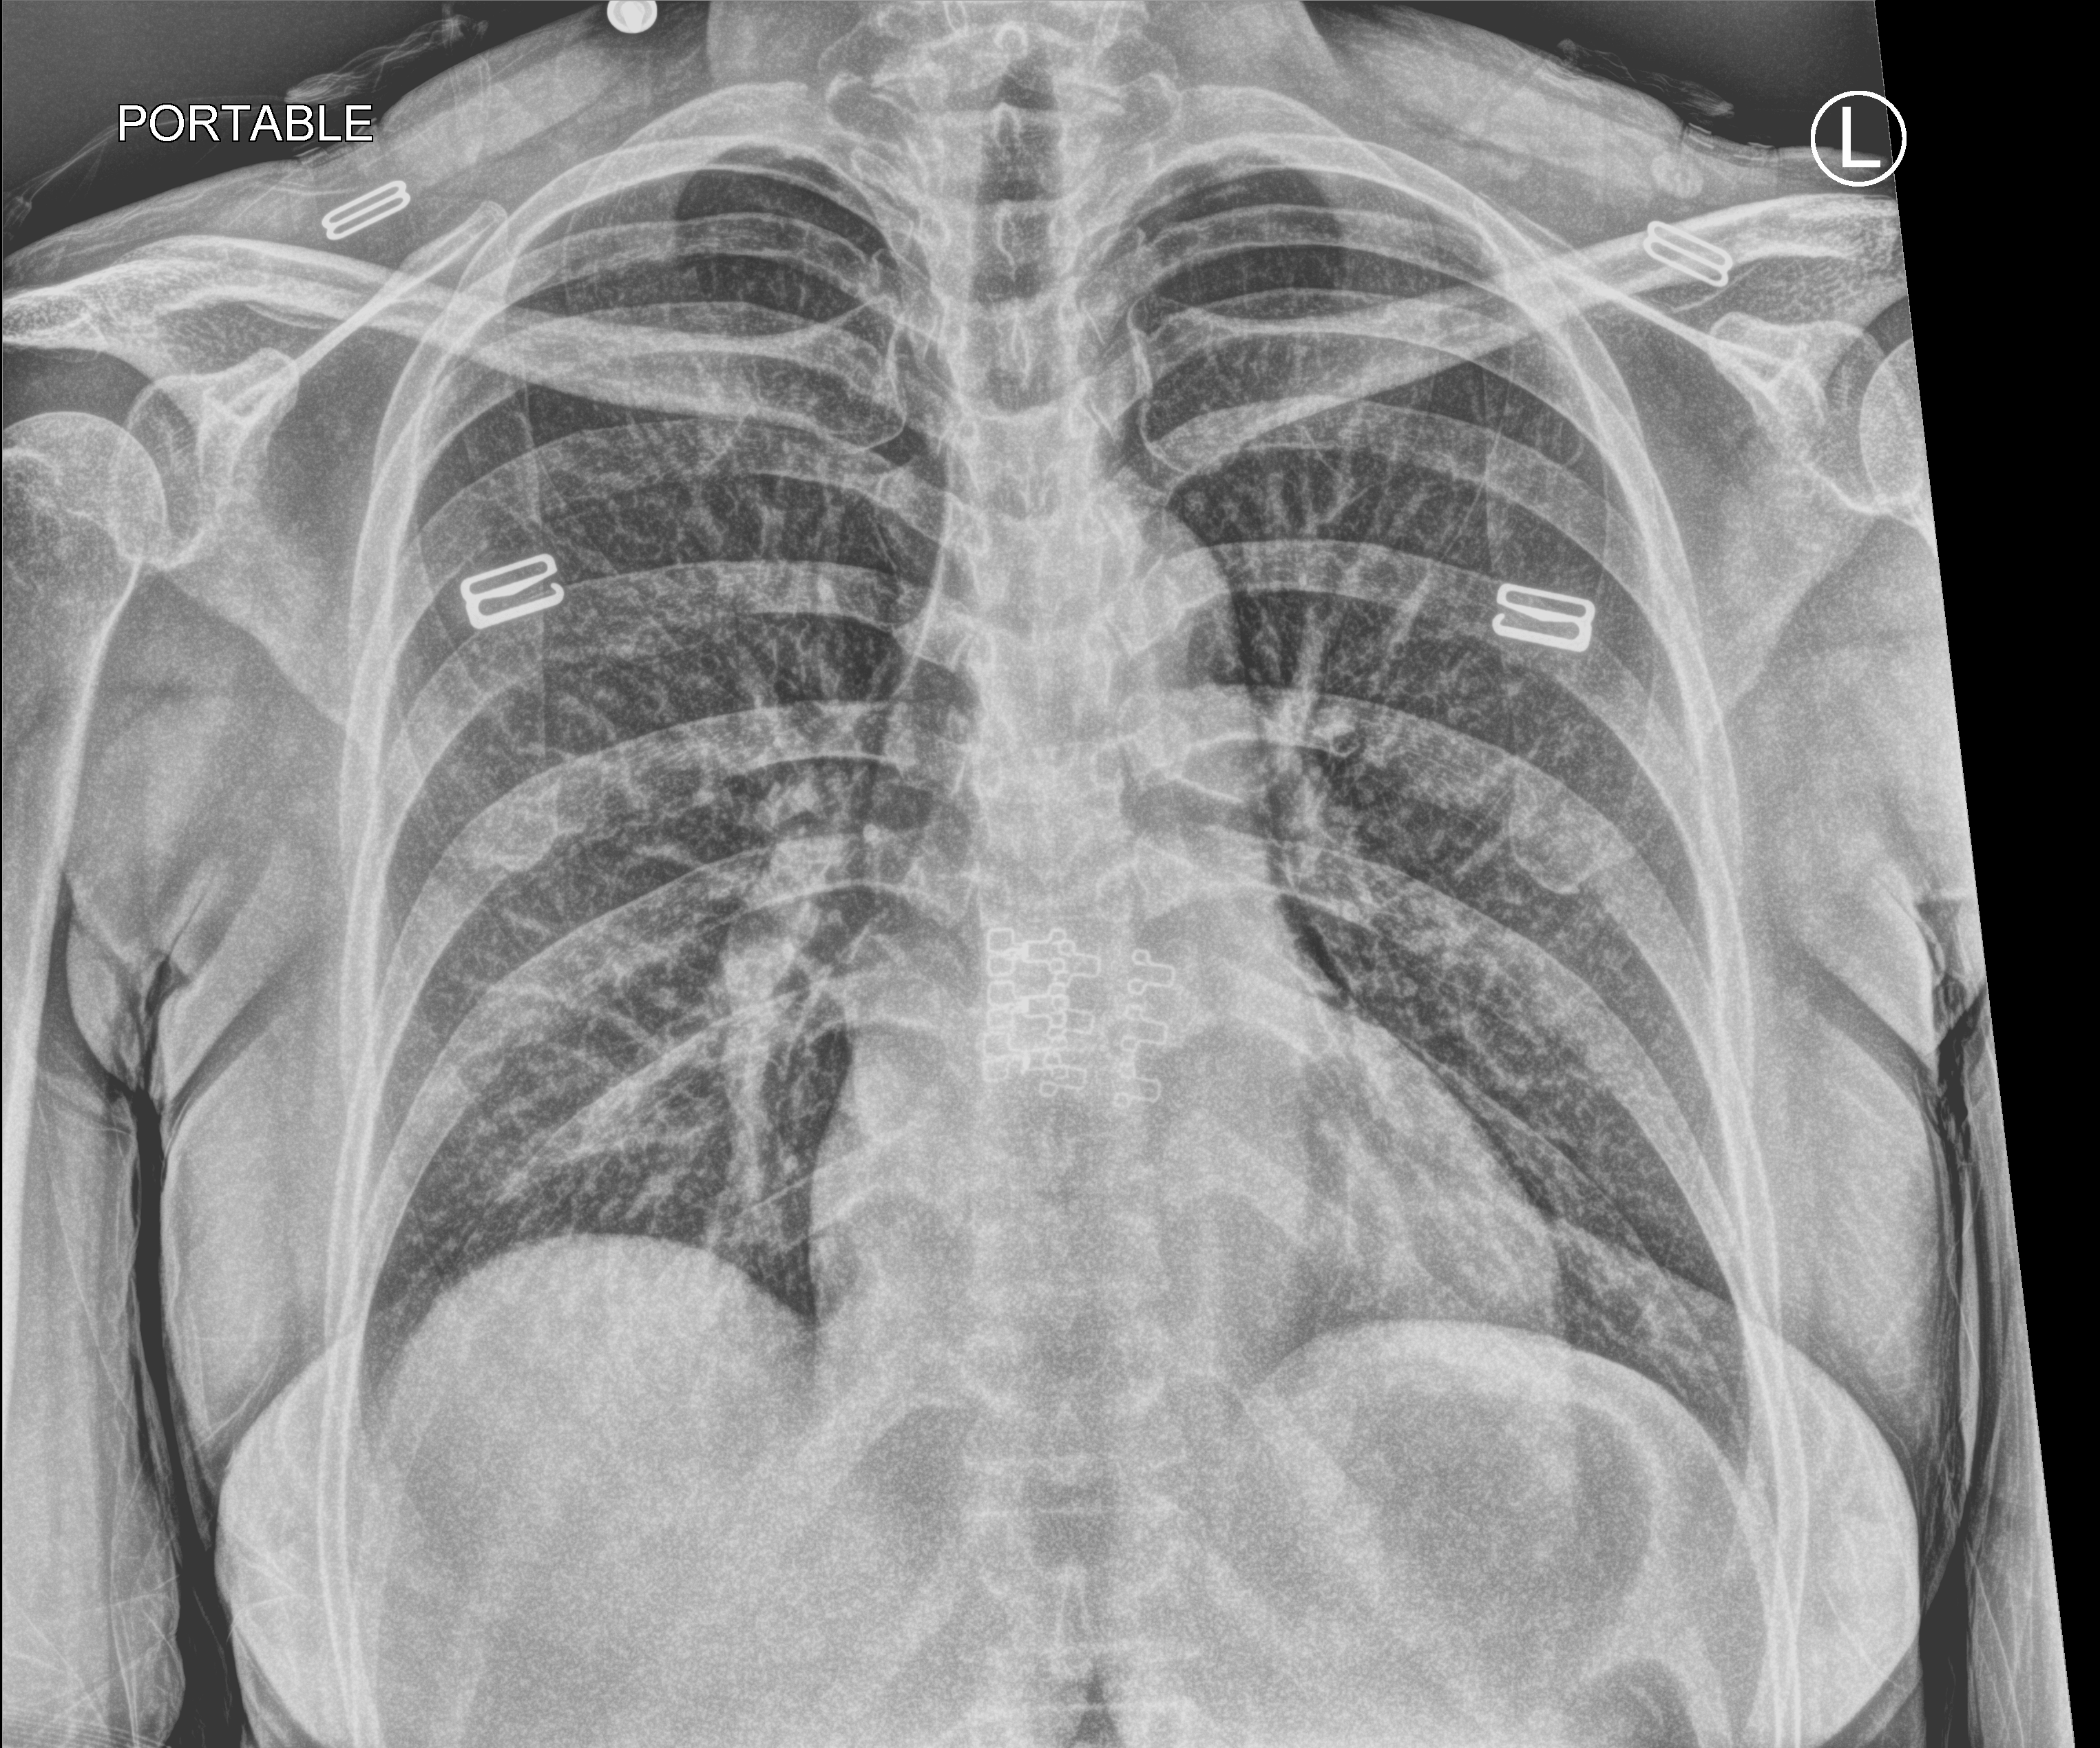
Chest X-ray (portable), anteroposterior (AP) projection. Female patient hospitalised with COVID-19, age 18–59 years.
Admission-level facts for this patient (not findings on this image; timing relative to this image not recorded): length of hospital stay: 2 days; admitted to intensive care during this hospital stay: no; smoking status (admission record): never.